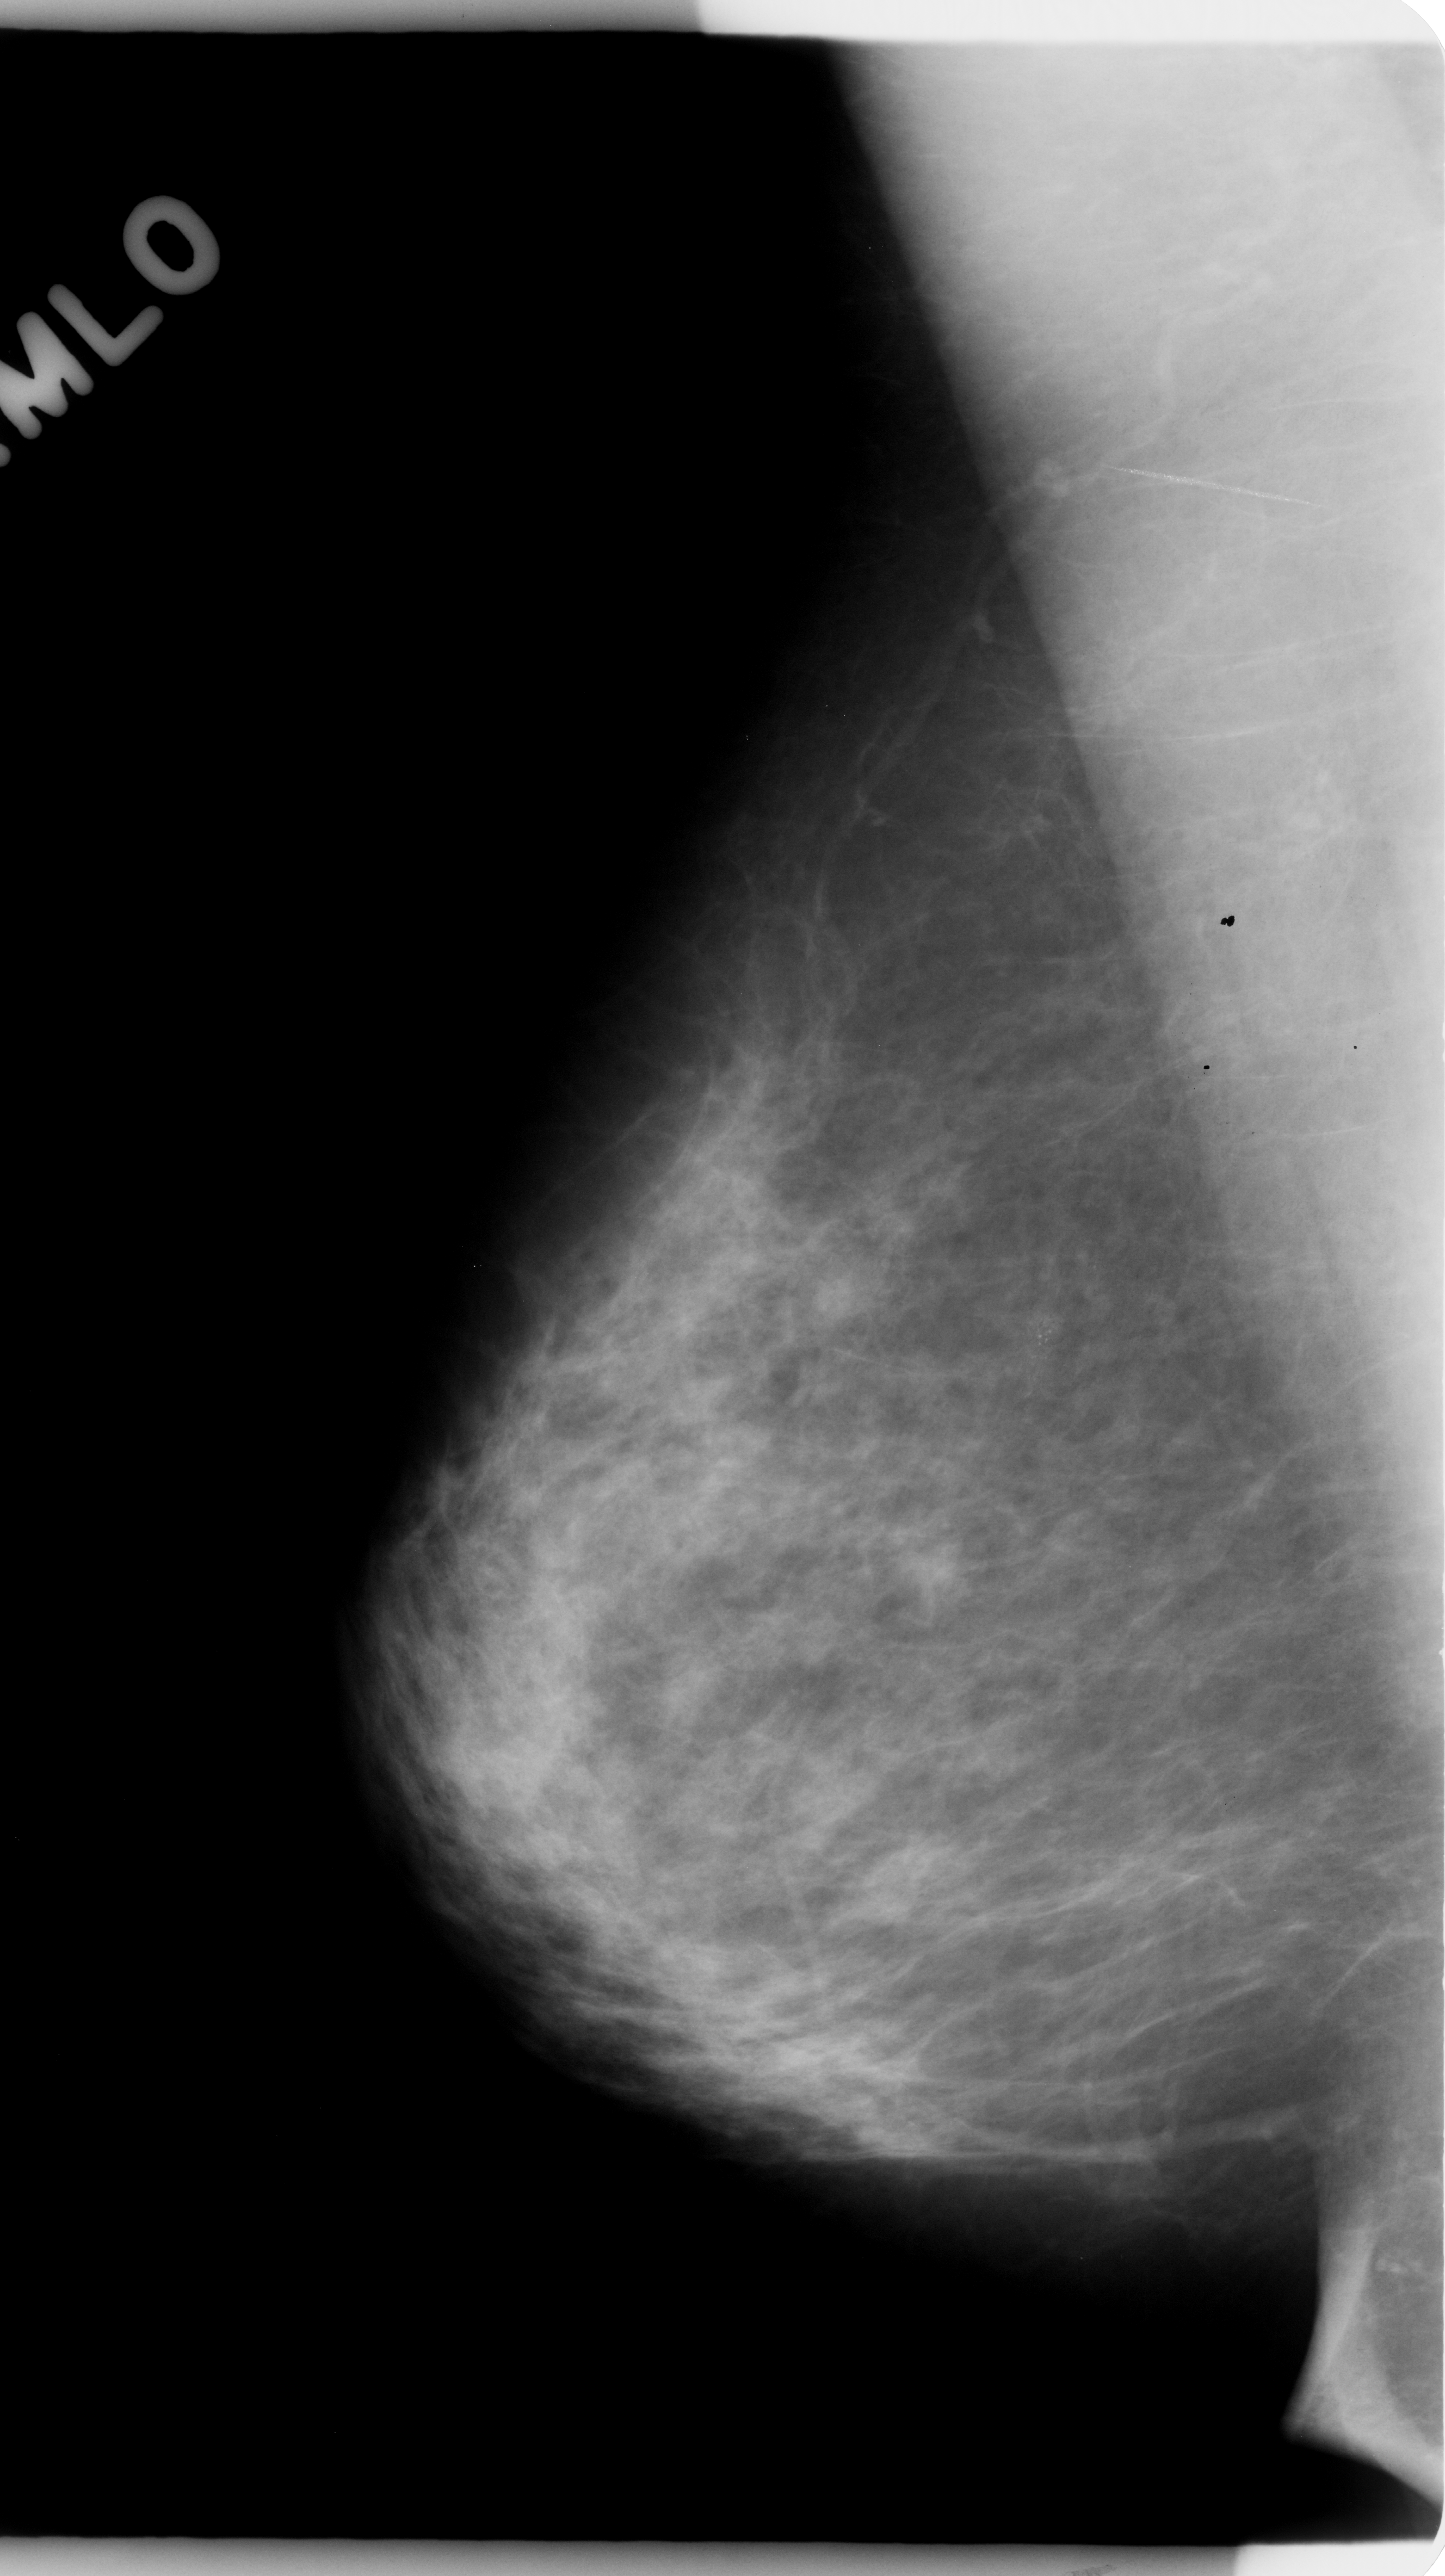
Digitized screen-film mammogram; right breast; mediolateral oblique (MLO) view; breast composition: scattered fibroglandular densities (BI-RADS density category 2 of 4); 1445 × 2576 image matrix.
Expert-marked regions of interest on this image (one box per marked abnormality):
- calcifications, morphology pleomorphic, distribution clustered; BI-RADS assessment category 4; pathology result (as recorded, not read from the image): malignant: bounding box <979,1135,1163,1398> (left, top, right, bottom; pixels)